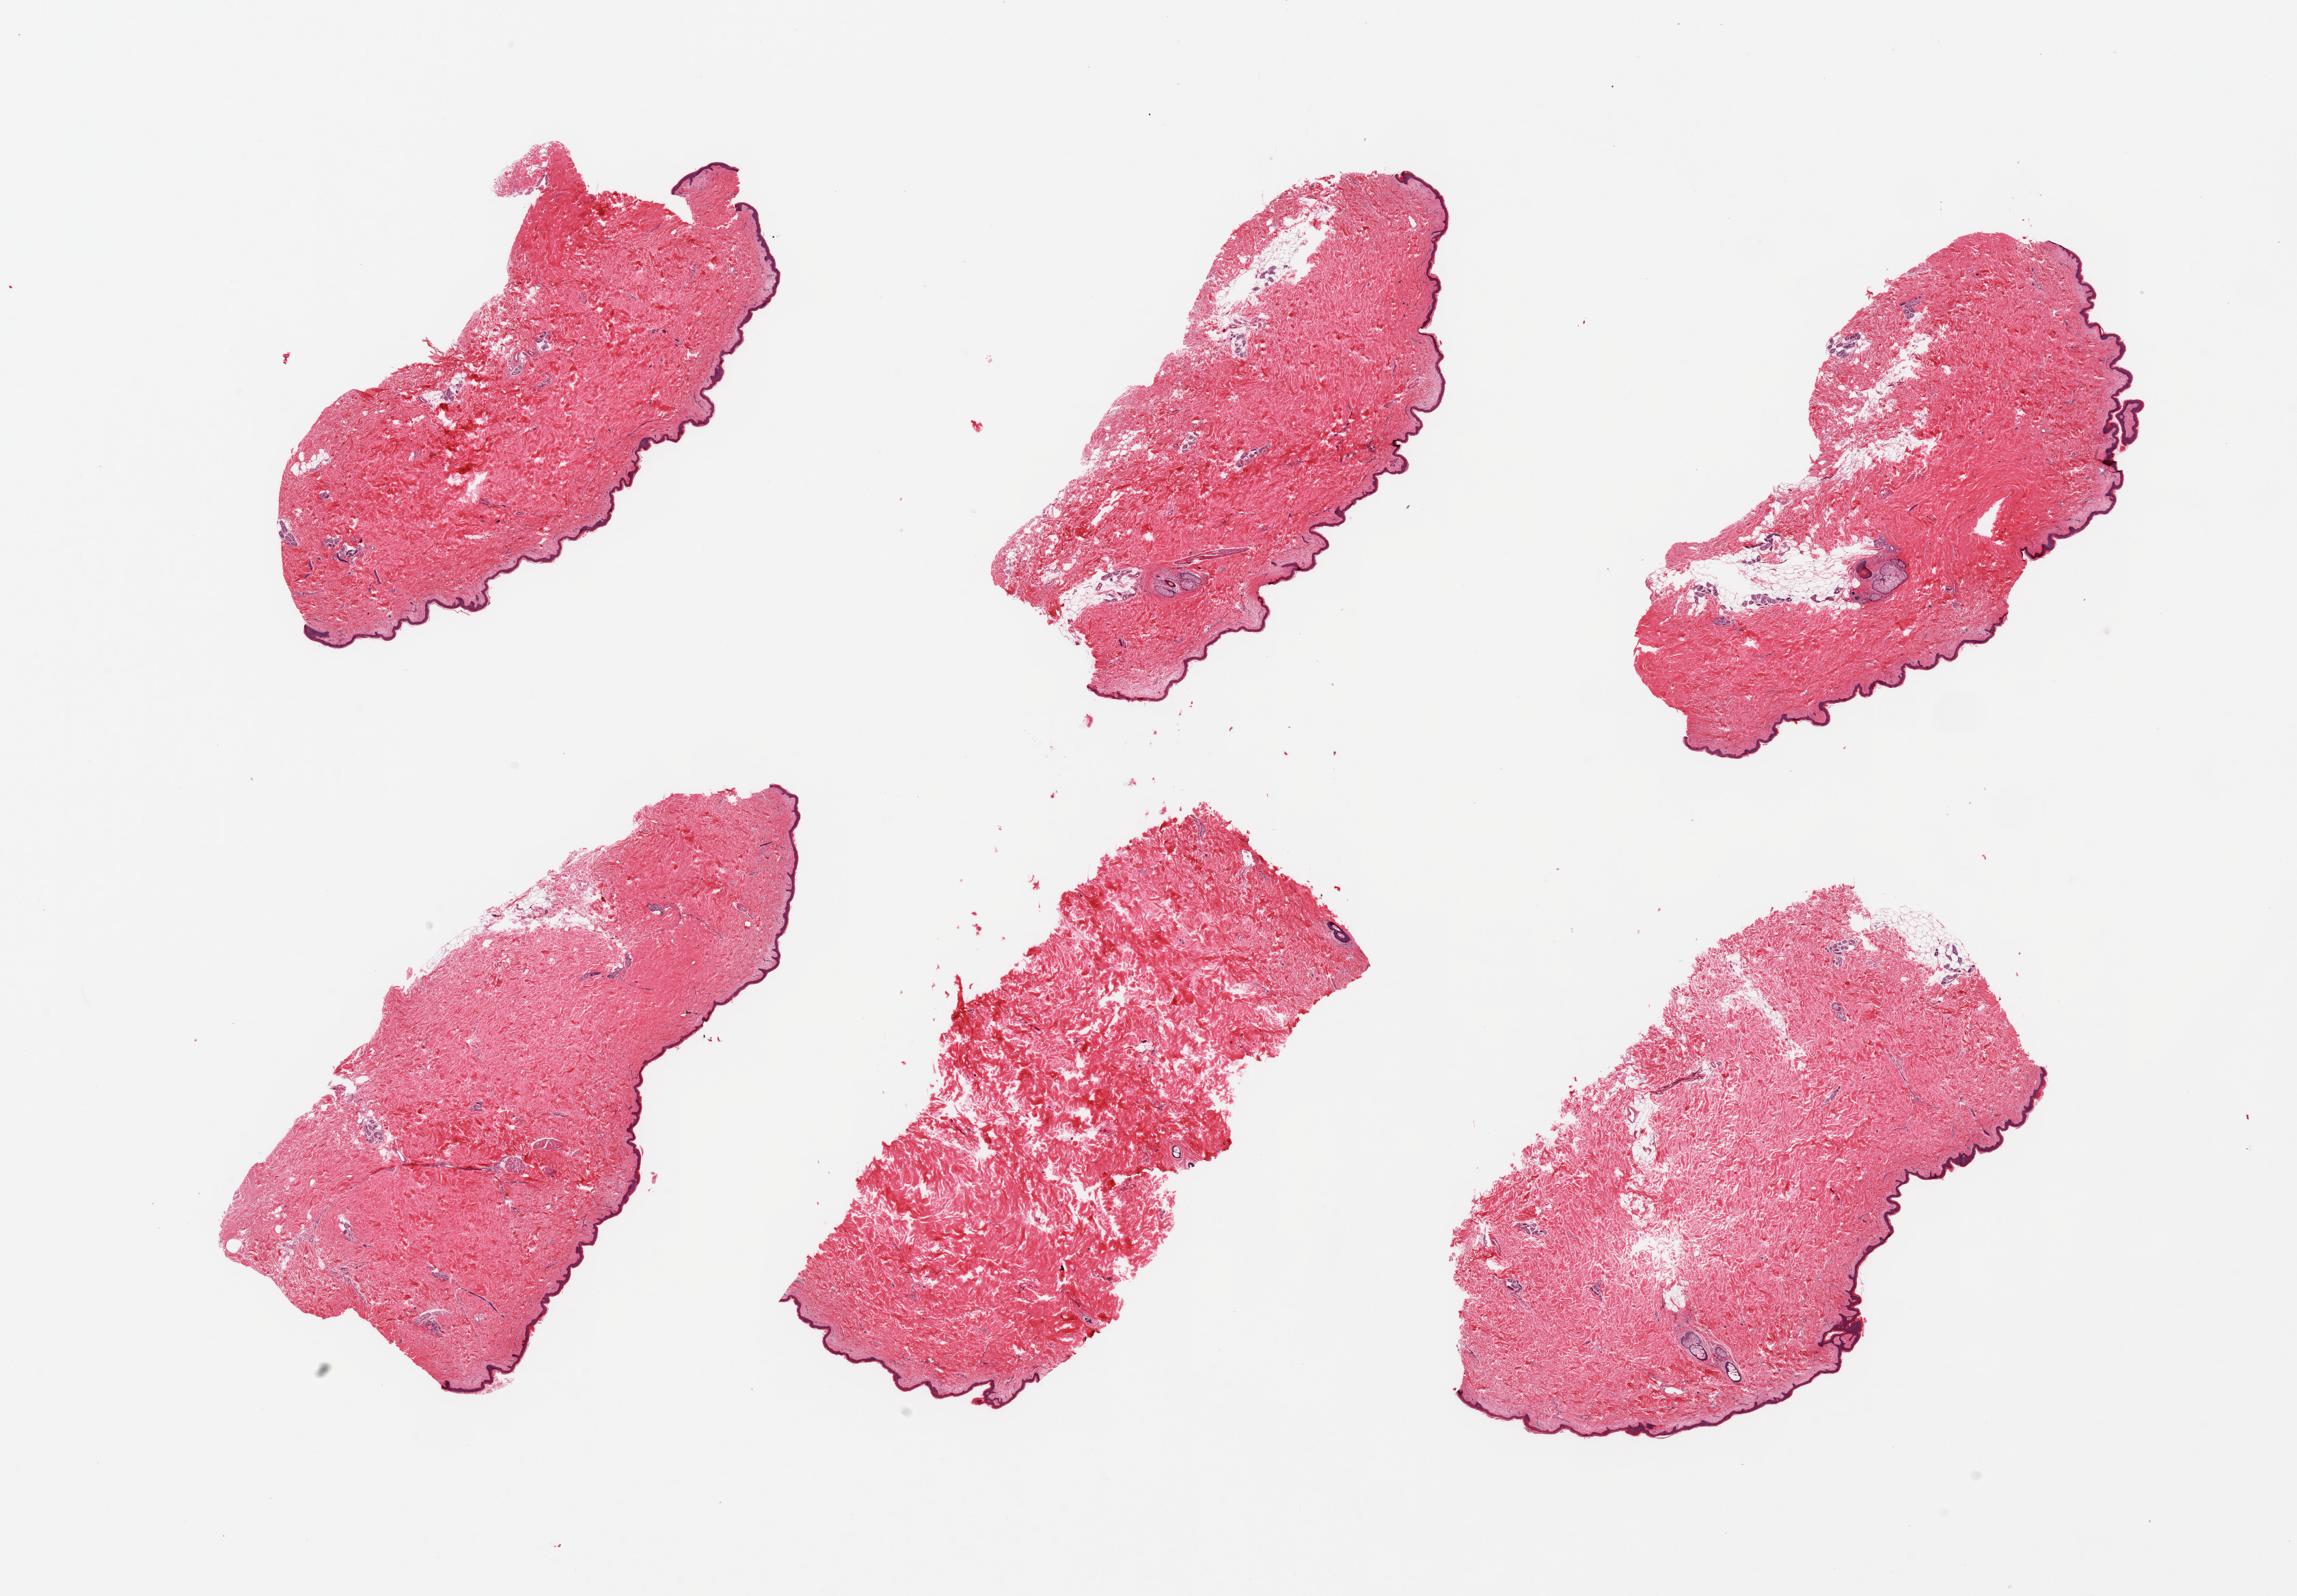
Whole-slide image, haematoxylin and eosin stain — a low-resolution overview of the entire scanned area, about 26.6 x 18.5 mm, PAXgene-fixed paraffin-embedded (PFPE) section, section of skin of suprapubic region (target tissue), donor tissue sample. Donor sex: female.
• pathologist's review note for this sample: 6 pieces, trace dermal fat; squamous epithelium is~25-35 microns